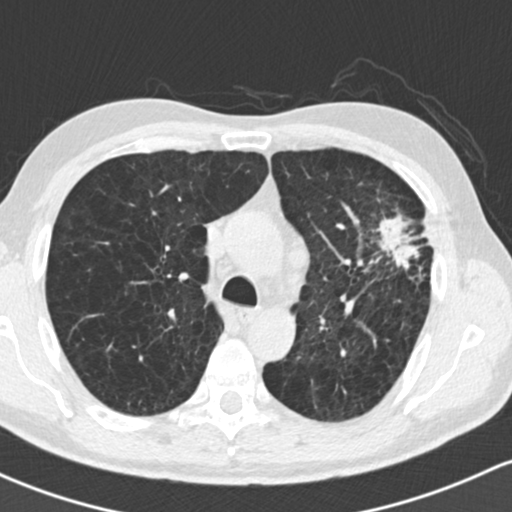
Axial slice from a low-dose chest CT screening exam. Baseline screening round. Lung window (W 1500 / L -600 HU). 120 kVp. Slice 55 of 162 in the series. 512 × 512 image matrix, field of view 318 × 318 mm. Male participant, aged 61 years at enrolment. Former smoker at enrolment.
• Lesion marked by an expert reader, bounding box <354,185,448,291> (left, top, right, bottom; pixels).
• Reader record for this screening exam (exam-level; its link to the box is not recorded): non-calcified nodule or mass ≥4 mm, left upper lobe, 35 × 35 mm, spiculated (stellate) margins, soft tissue attenuation.
• Later outcome: lung cancer diagnosed 19 days after this screen — adenocarcinoma, NOS, left upper lobe, well differentiated (G1), stage IIIA (AJCC 6th edition), 45 mm at pathology.